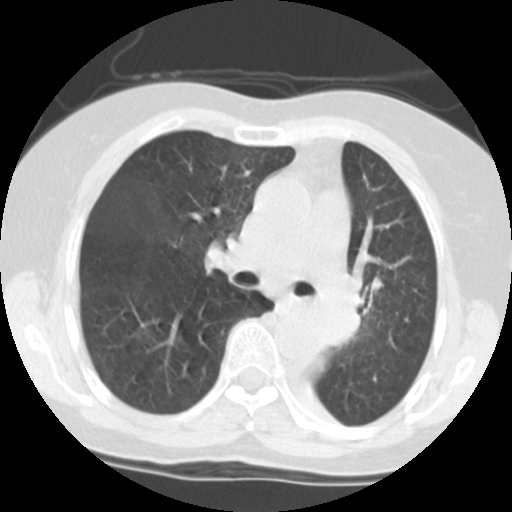
Low-dose screening chest CT, one axial slice. Slice 74 of 113 in the series (ordered by position). 140 kVp. Lung window (W 1500 / L -600 HU). 512 × 512 image matrix, field of view 280 × 280 mm.
Structures marked on this image (outlined manually by an expert reader):
- lesion 1 (tumor, left main bronchus): box from (x=297, y=299) to (x=362, y=345) px